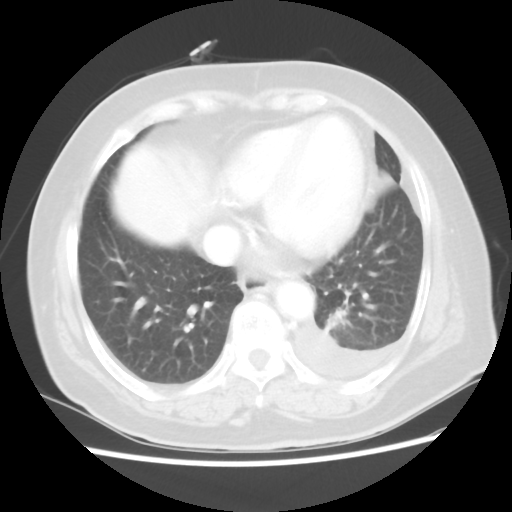
Chest CT, one axial slice. Slice 20 of 80 in the series (ordered by position). Reconstruction kernel STANDARD. 100 kVp. Lung window (W 1500 / L -600 HU). 512 × 512 image matrix, field of view 343 × 343 mm. Female patient, age 68 years. From the clinical record (not read from this slice): clinical TNM (as recorded): T1c N0 M1.
Outlined on this slice (rectangle marked by the reading radiologist):
- lung tumour (recorded histology: adenocarcinoma): bounding box <319,304,355,338> (left, top, right, bottom; pixels)